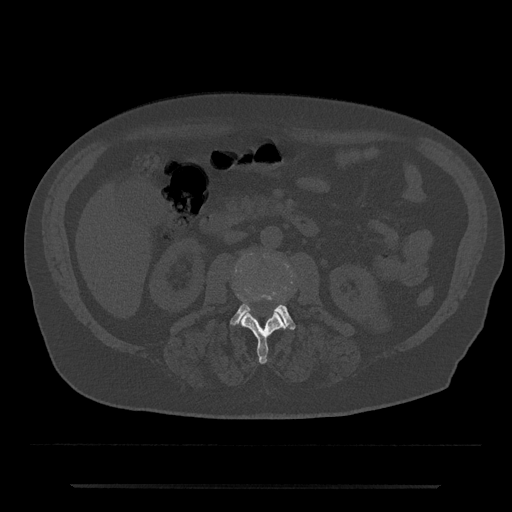
CT including the spine, one axial slice. Position 443 of 797 along the scan axis. 120 kVp. Bone window (W 1800 / L 400 HU). 0.5 mm slice thickness. 512 × 512 image matrix, field of view 434 × 434 mm. Patient: male, 80 years. From the clinical record (not read from this slice): primary cancer: prostate; vertebrae with lytic lesions (as recorded): L1, T11.
Annotated regions visible in this slice (semi-automatically segmented with operator editing):
- L2 vertebra: bounding box (x1, y1, x2, y2) in pixels: (241, 295, 288, 364)
- L3 vertebra: (230, 291, 296, 330)